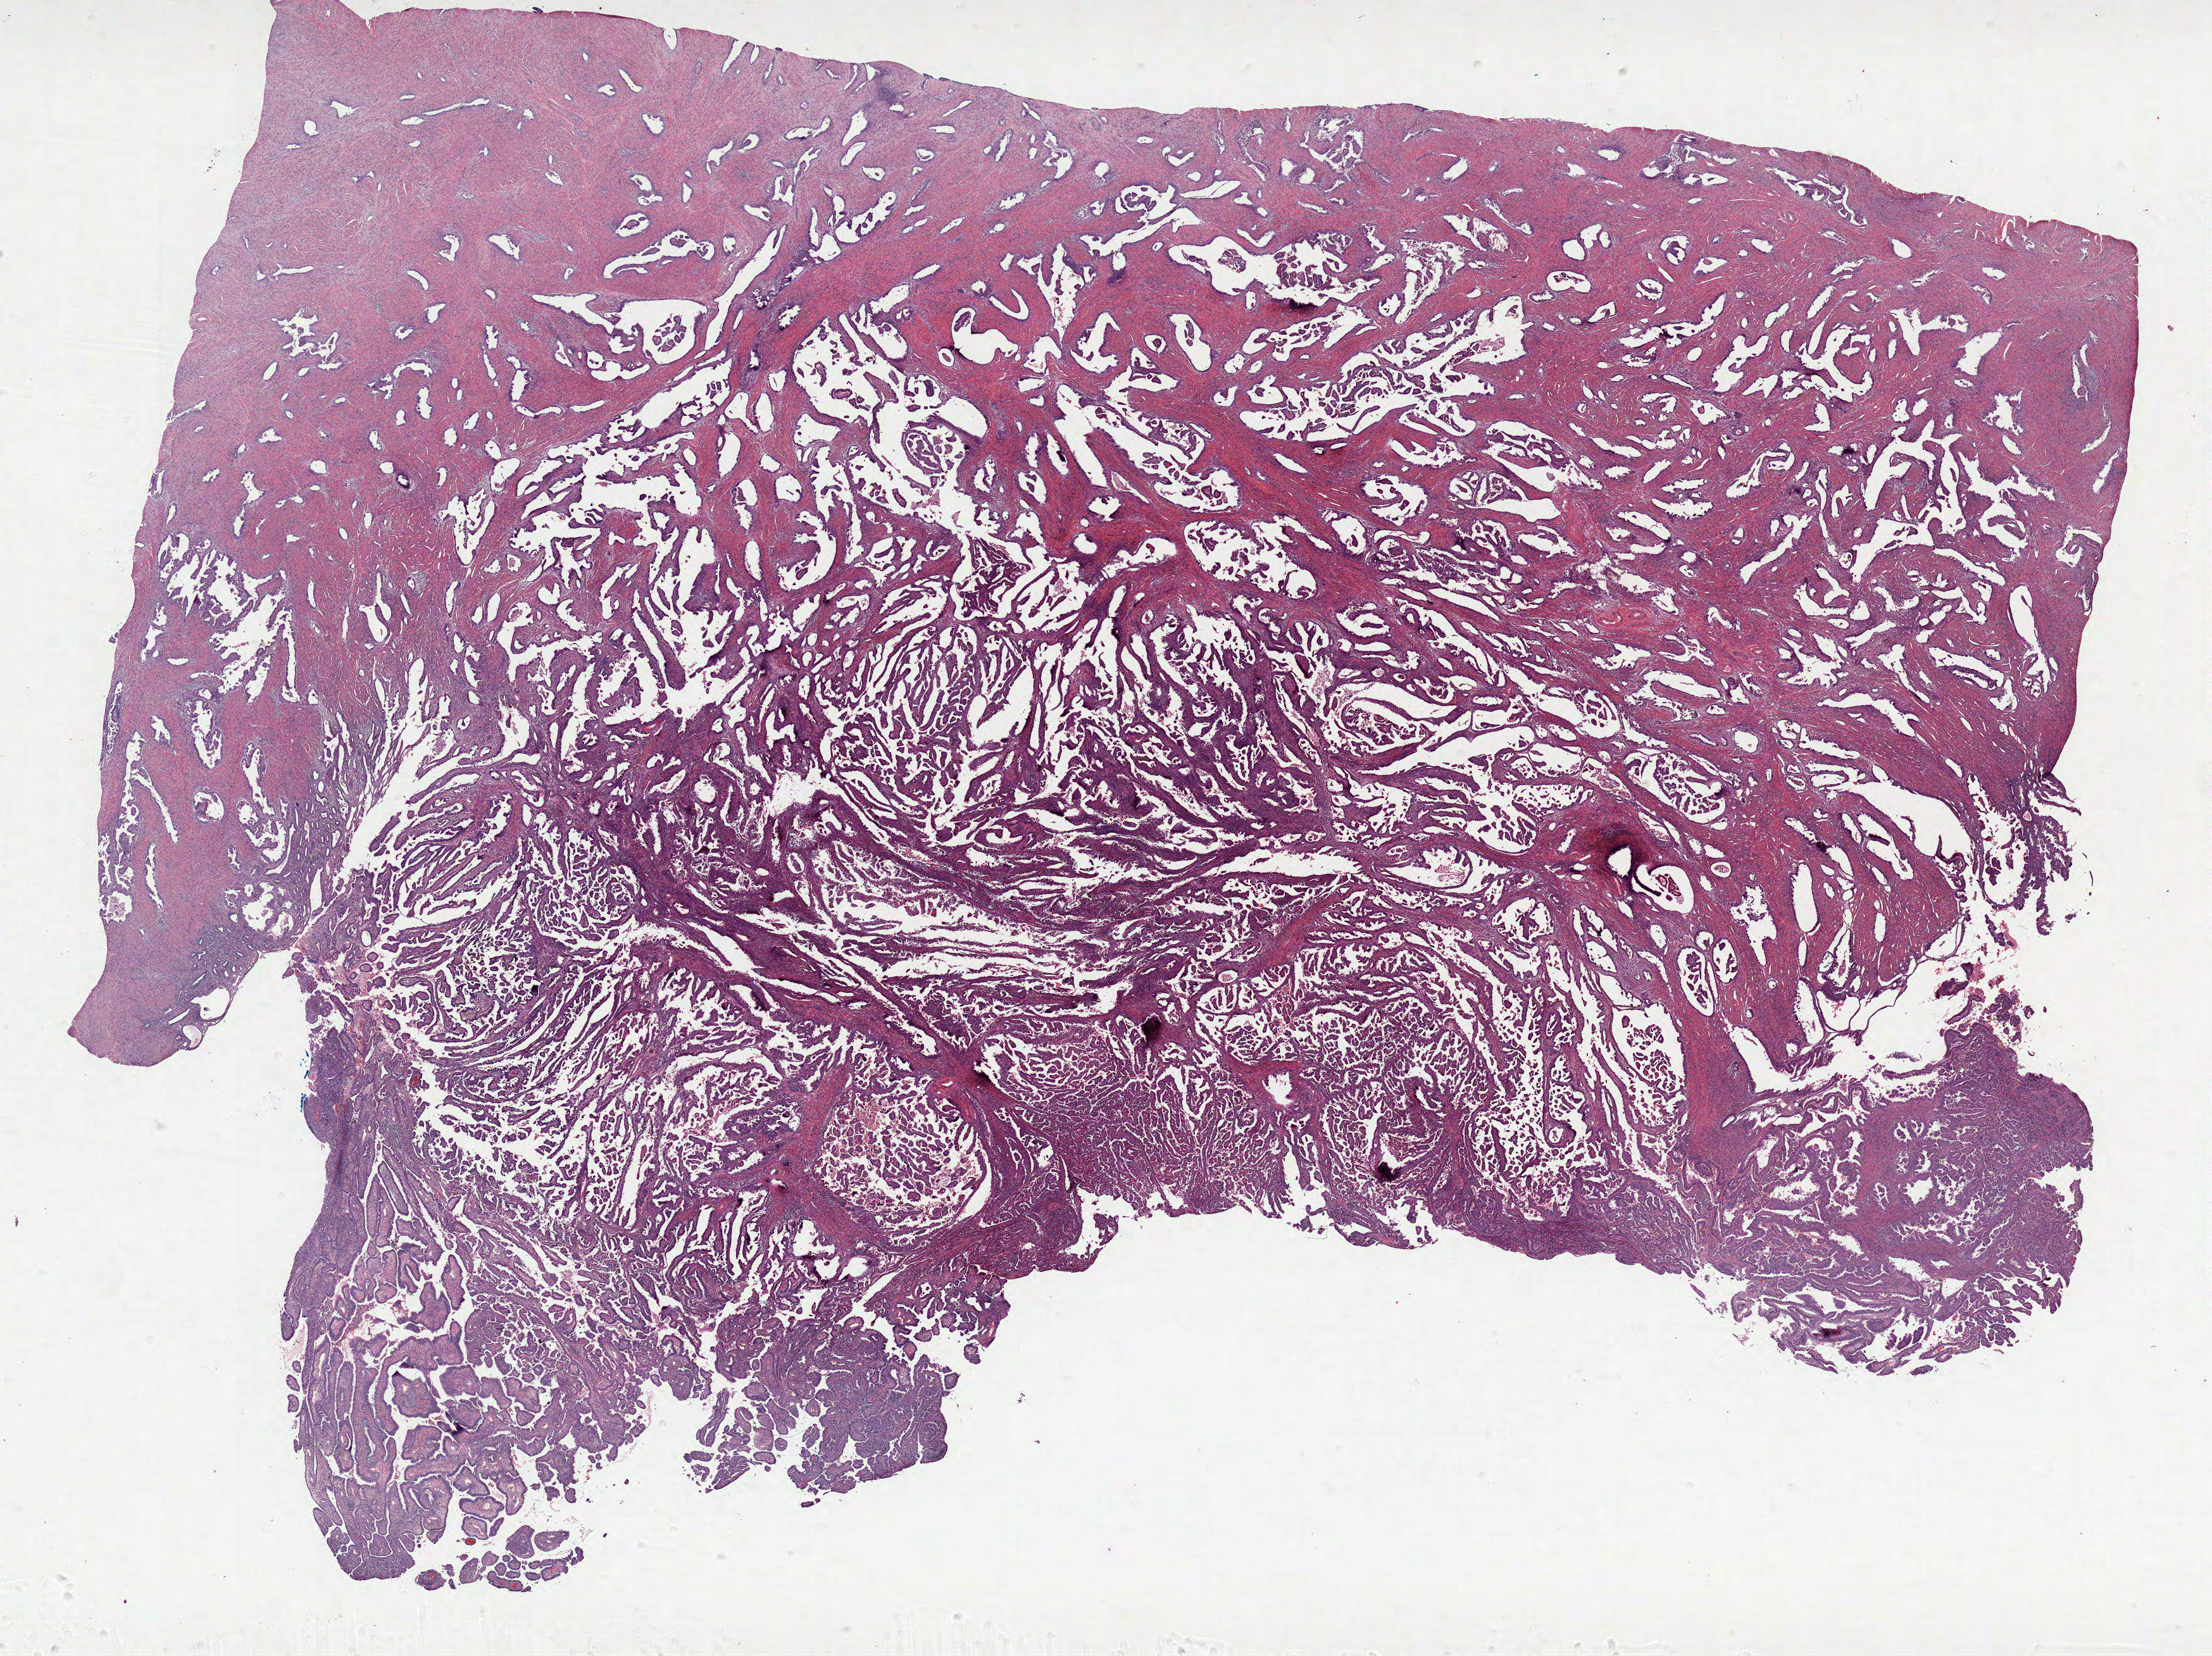
Digitized H&E tissue section (whole slide), low-resolution overview of the scanned area, about 27.8 x 20.8 mm (slide scanned at 20x). FFPE section. Uterus, primary tumour sample. Patient: female, age at initial diagnosis 76 years. Histologic grade: high grade.
FIGO stage: IIIC1. Lymph nodes positive (case pathology): 6 of 20 examined. Histologic diagnosis: Endometrioid adenocarcinoma, NOS (endometrium).